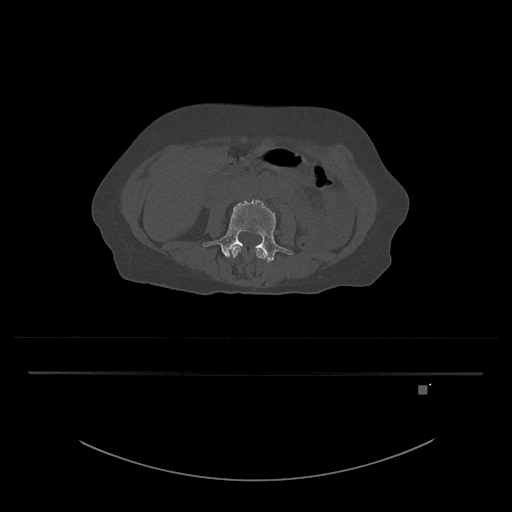
CT including the spine, one axial slice. Slice 379 of 797 in the series (ordered by position). Reconstruction kernel Br40s/3. Bone window (W 1800 / L 400 HU). 512 × 512 image matrix. Patient: female, 57 years. Case-level facts recorded for this patient, not image findings: primary cancer: cervical.
Annotated regions visible in this slice (semi-automatic segmentation, software-assisted and operator-edited):
- L3 vertebra: bounding box (x1, y1, x2, y2) in pixels: (231, 245, 267, 260)
- L4 vertebra: (203, 199, 293, 263)